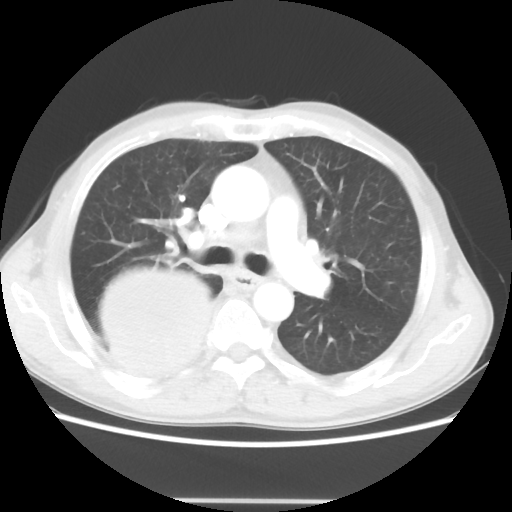
Chest CT, one axial slice. Position 30 of 48 along the scan axis. Reconstruction kernel STANDARD. Lung window (W 1500 / L -600 HU). 512 × 512 image matrix, field of view 361 × 361 mm. Male patient, age 66 years. Case-level facts recorded for this patient, not image findings: clinical TNM (as recorded): T4 N1 M1; histopathological grade: G3.
Annotated regions visible in this slice (rectangle marked by the reading radiologist):
- lung tumour (recorded histology: small cell carcinoma): bounding box <84,264,219,381> (left, top, right, bottom; pixels)